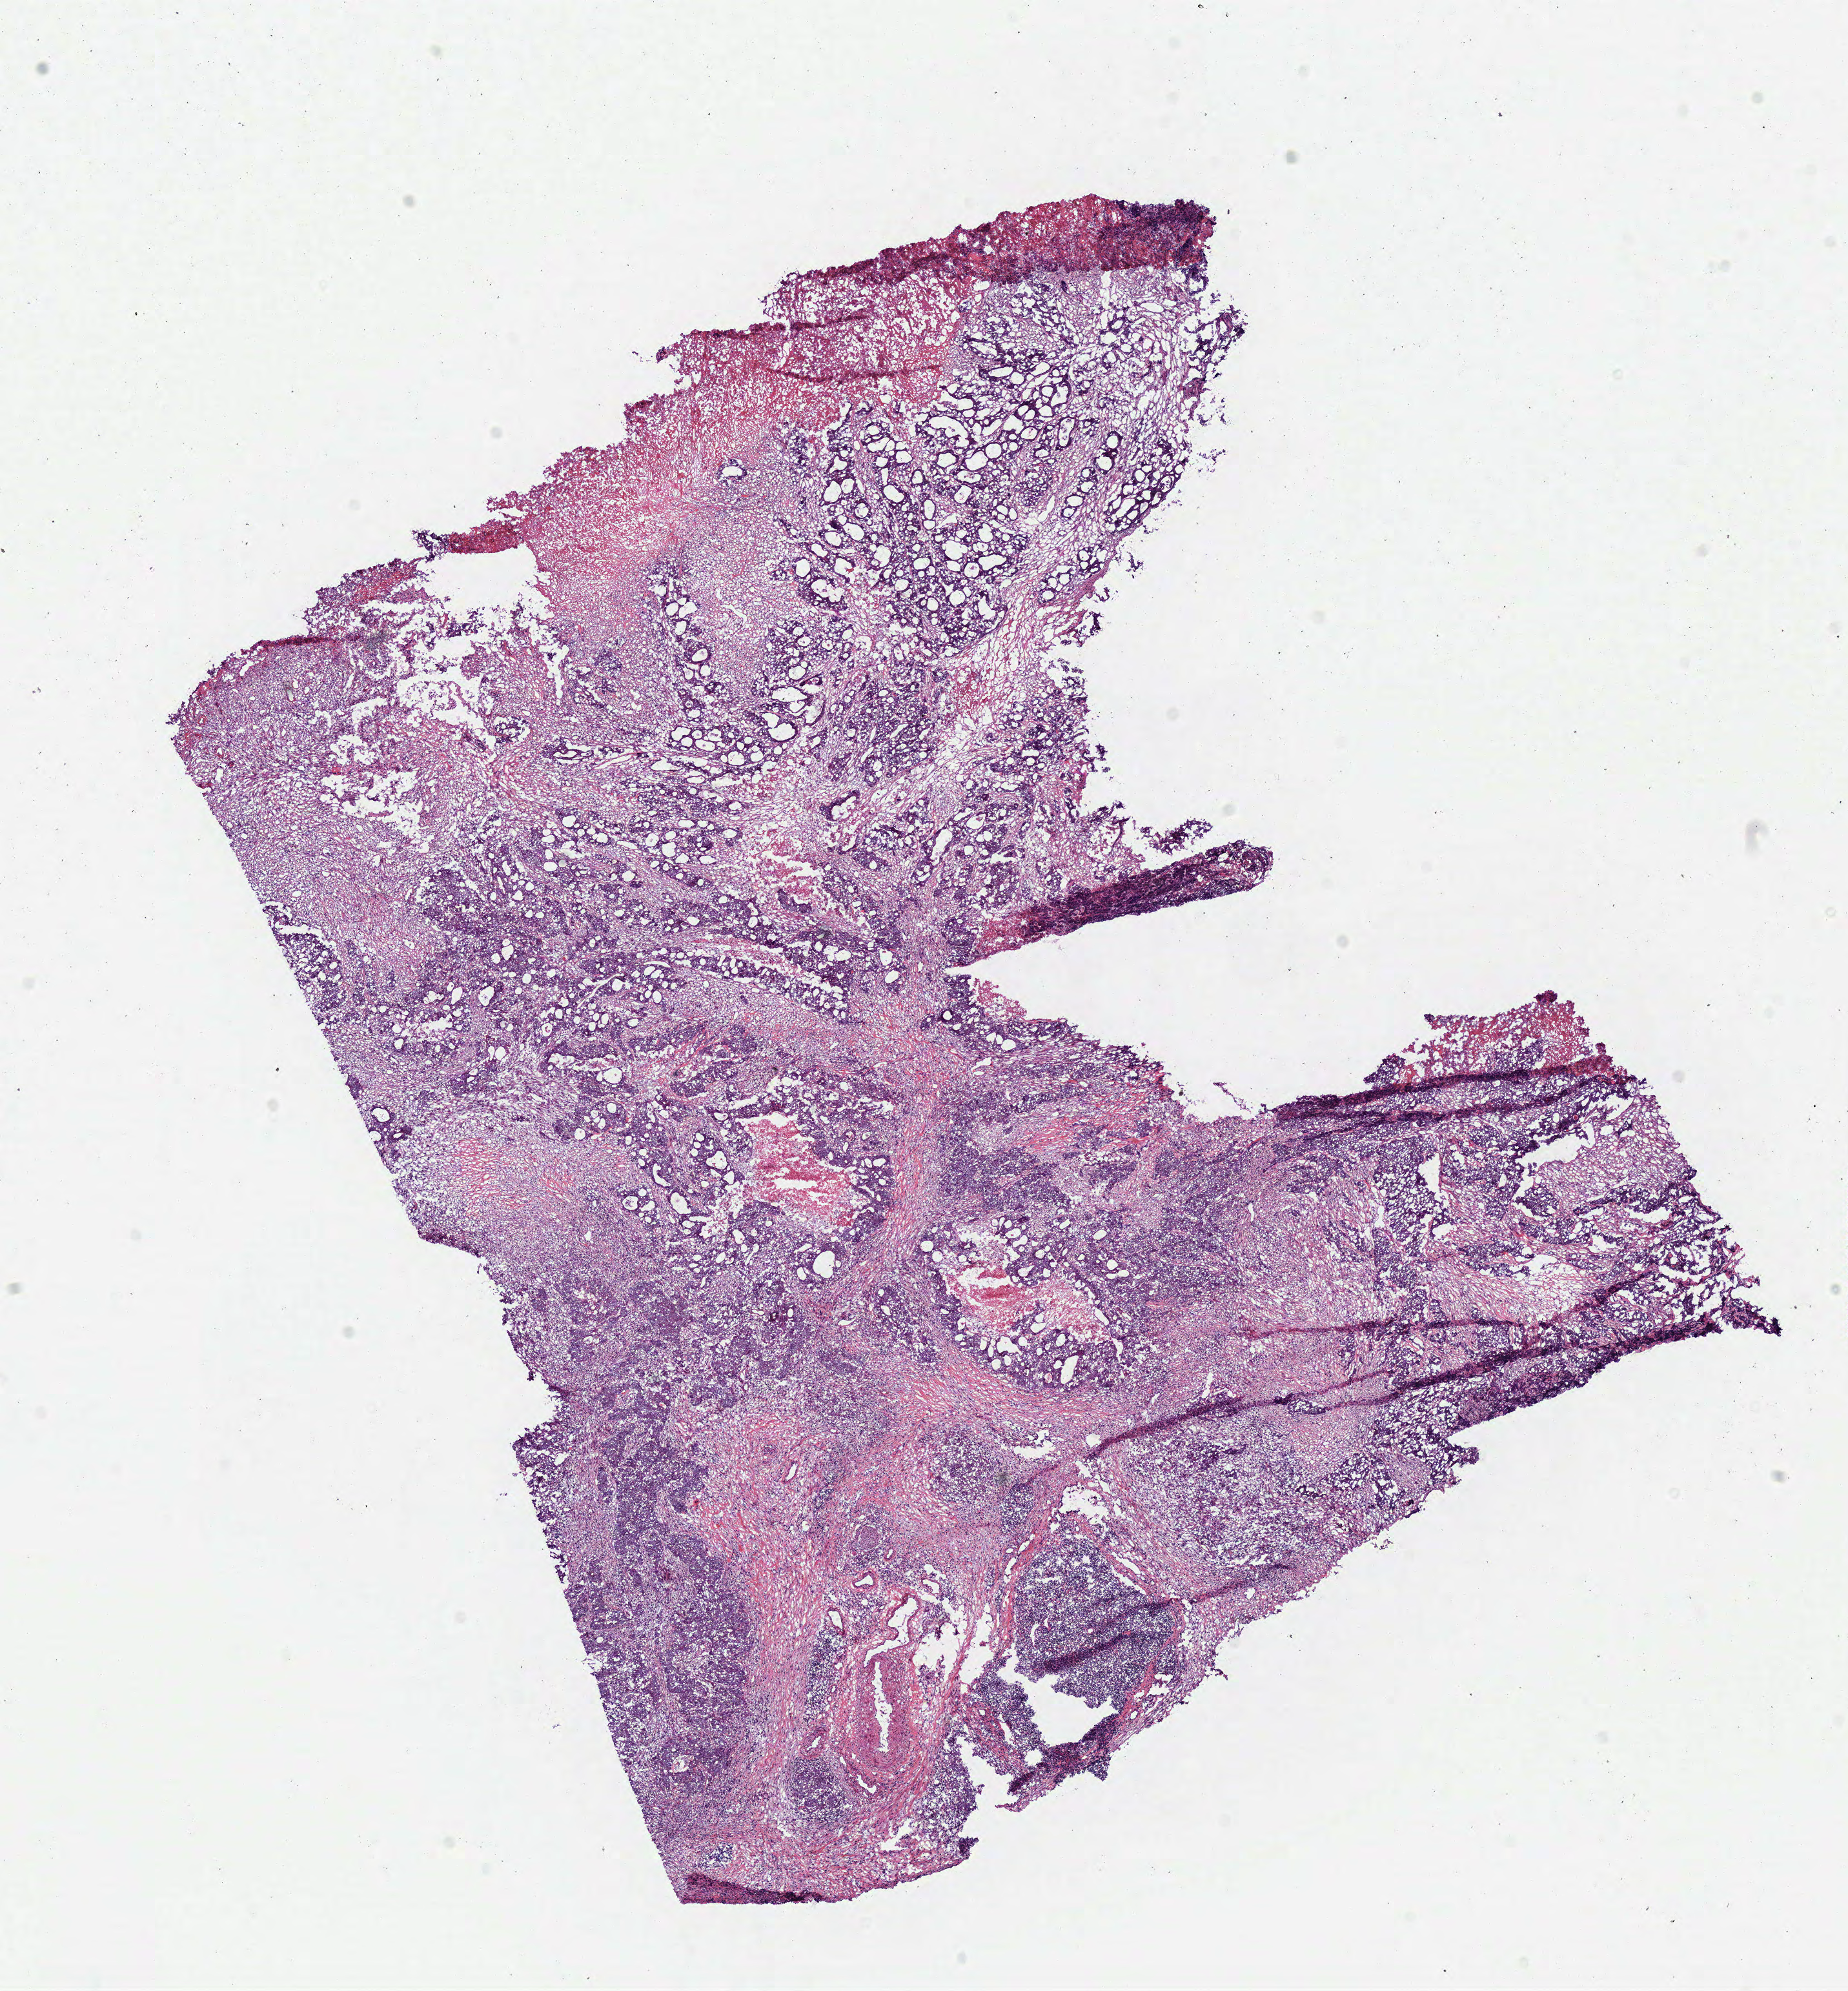
H&E-stained whole-slide image, shown as a low-resolution overview of the whole scanned area (about 11.3 x 12.1 mm, acquisition: 40x scan). Frozen section from the bottom of the tissue portion. Colon, primary tumour sample. Patient: female, age at initial diagnosis 66 years. Composition of this section per pathologist review: tumour cells 65%, tumour nuclei 80%, normal cells 0%, stromal cells 30%, necrosis 5%.
Histologic diagnosis: Adenocarcinoma, NOS (transverse colon). Lymph nodes positive (case pathology): 0 of 25 examined. AJCC pathologic stage: IIB (6th edition).